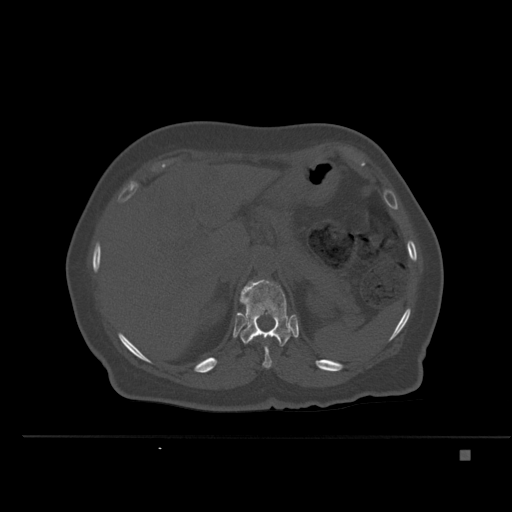
CT including the spine, one axial slice; slice 256 of 477 in the series (ordered by position); bone window (W 1800 / L 400 HU); 512 × 512 image matrix. Female patient, age 74 years. Case-level facts recorded for this patient, not image findings: primary cancer: colon.
Annotated regions visible in this slice (semi-automatic segmentation, software-assisted and operator-edited):
- T11 vertebra: bounding box (x1, y1, x2, y2) in pixels: (253, 336, 275, 368)
- T12 vertebra: (240, 279, 291, 346)